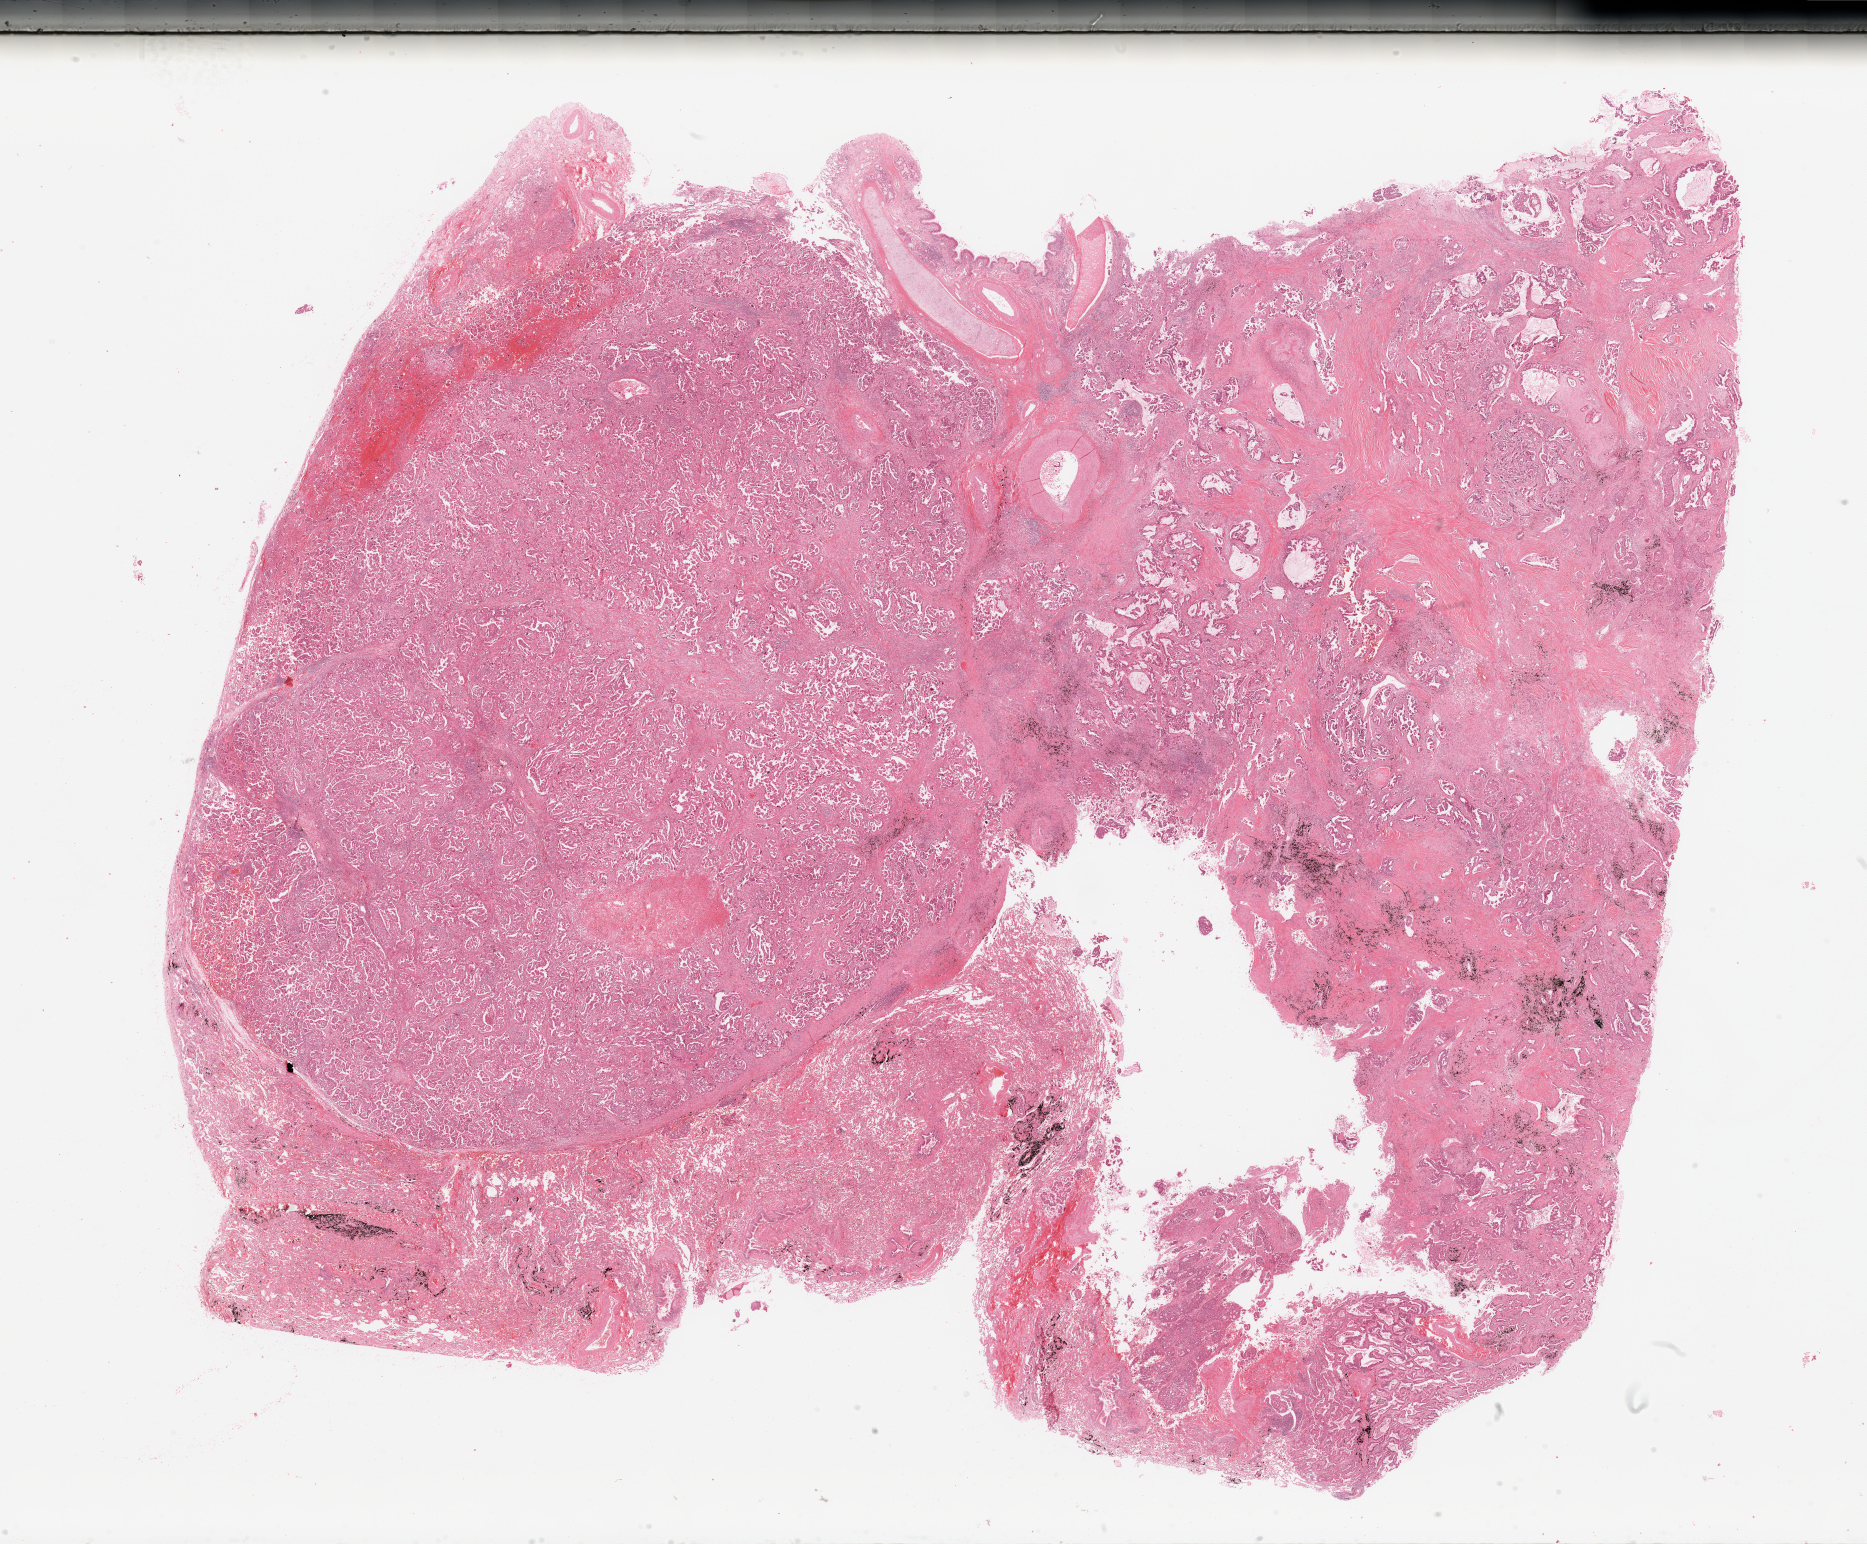
Whole-slide histology image, H&E-stained — whole scanned area (about 29.5 x 24.4 mm, slide scanned at 20x) shown as a low-resolution overview, lung, tumour tissue. Male, 63 y/o. Histologic grade: G2 (moderately differentiated).
• histologic diagnosis: Adenocarcinoma, NOS